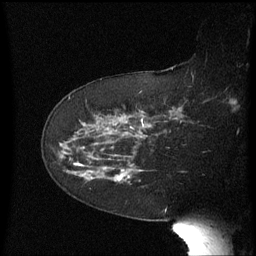
Breast MRI (dynamic contrast-enhanced), one sagittal slice; position 40 of 60 along the scan axis; dynamic contrast-enhanced series, image 2 of 3 at this slice position (ordered by acquisition); 1.5 T; TE 4.2 ms, TR 8.4 ms; 2.3 mm slice thickness; 256 × 256 image matrix, field of view 200 × 200 mm. Female patient, age 63 years. Case-level facts recorded for this patient, not image findings: setting: breast cancer imaged before/during neoadjuvant chemotherapy; receptor status: HER2-positive.
Outlined on this slice (semi-automatically segmented with operator editing):
- analysis volume of interest (the breast-tissue region the enhancement analysis was run in; not a lesion): box from (x=66, y=136) to (x=138, y=185) px
- tumour enhancement mask (voxels above the 70 % enhancement threshold inside the analysis volume of interest): (x=76, y=164)–(x=127, y=181)